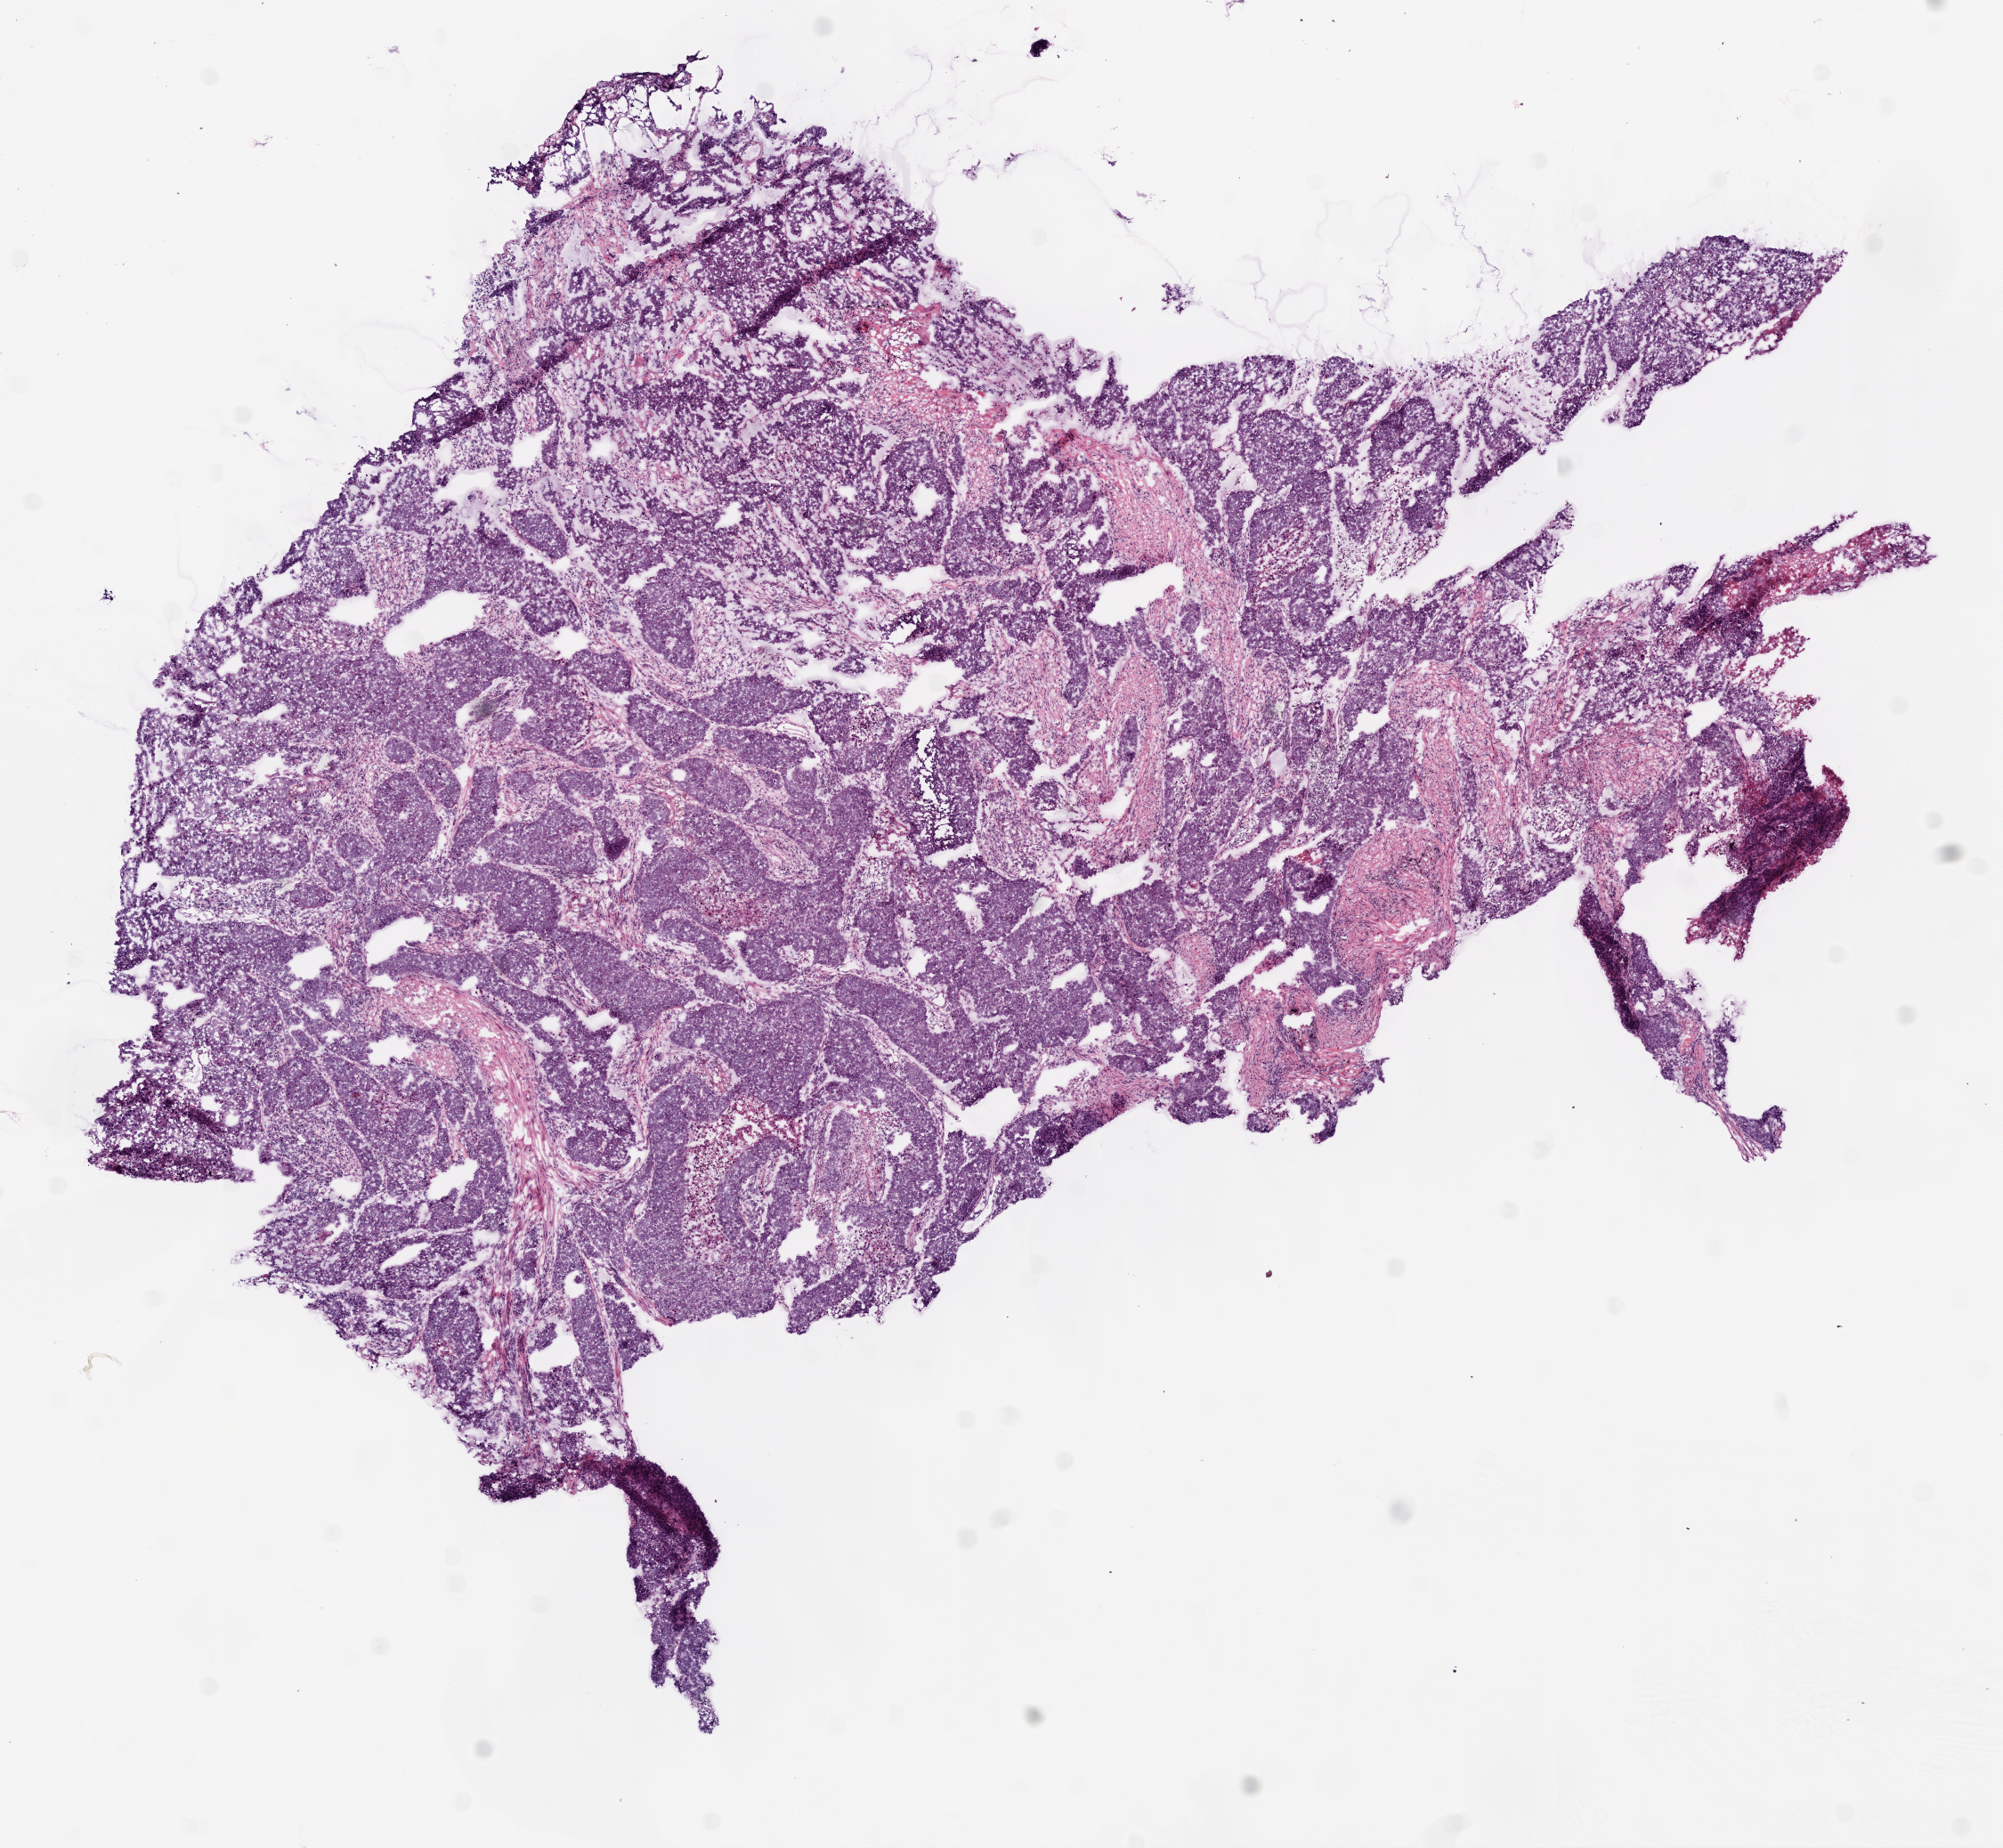
Hematoxylin and eosin (H&E) stained whole-slide image, shown as a low-resolution overview of the whole scanned area (about 9.0 x 8.3 mm). Frozen section from the bottom of the tissue portion. Primary tumour sample from the lung. Male, age 68 years at initial diagnosis. Slide review estimates, as recorded: tumour cells 73%, tumour nuclei 85%, normal cells 0%, stromal cells 12%, necrosis 15%.
Laterality: left. Pathologic diagnosis: Squamous cell carcinoma, NOS (upper lobe, lung). AJCC pathologic stage: IIIB (6th edition).